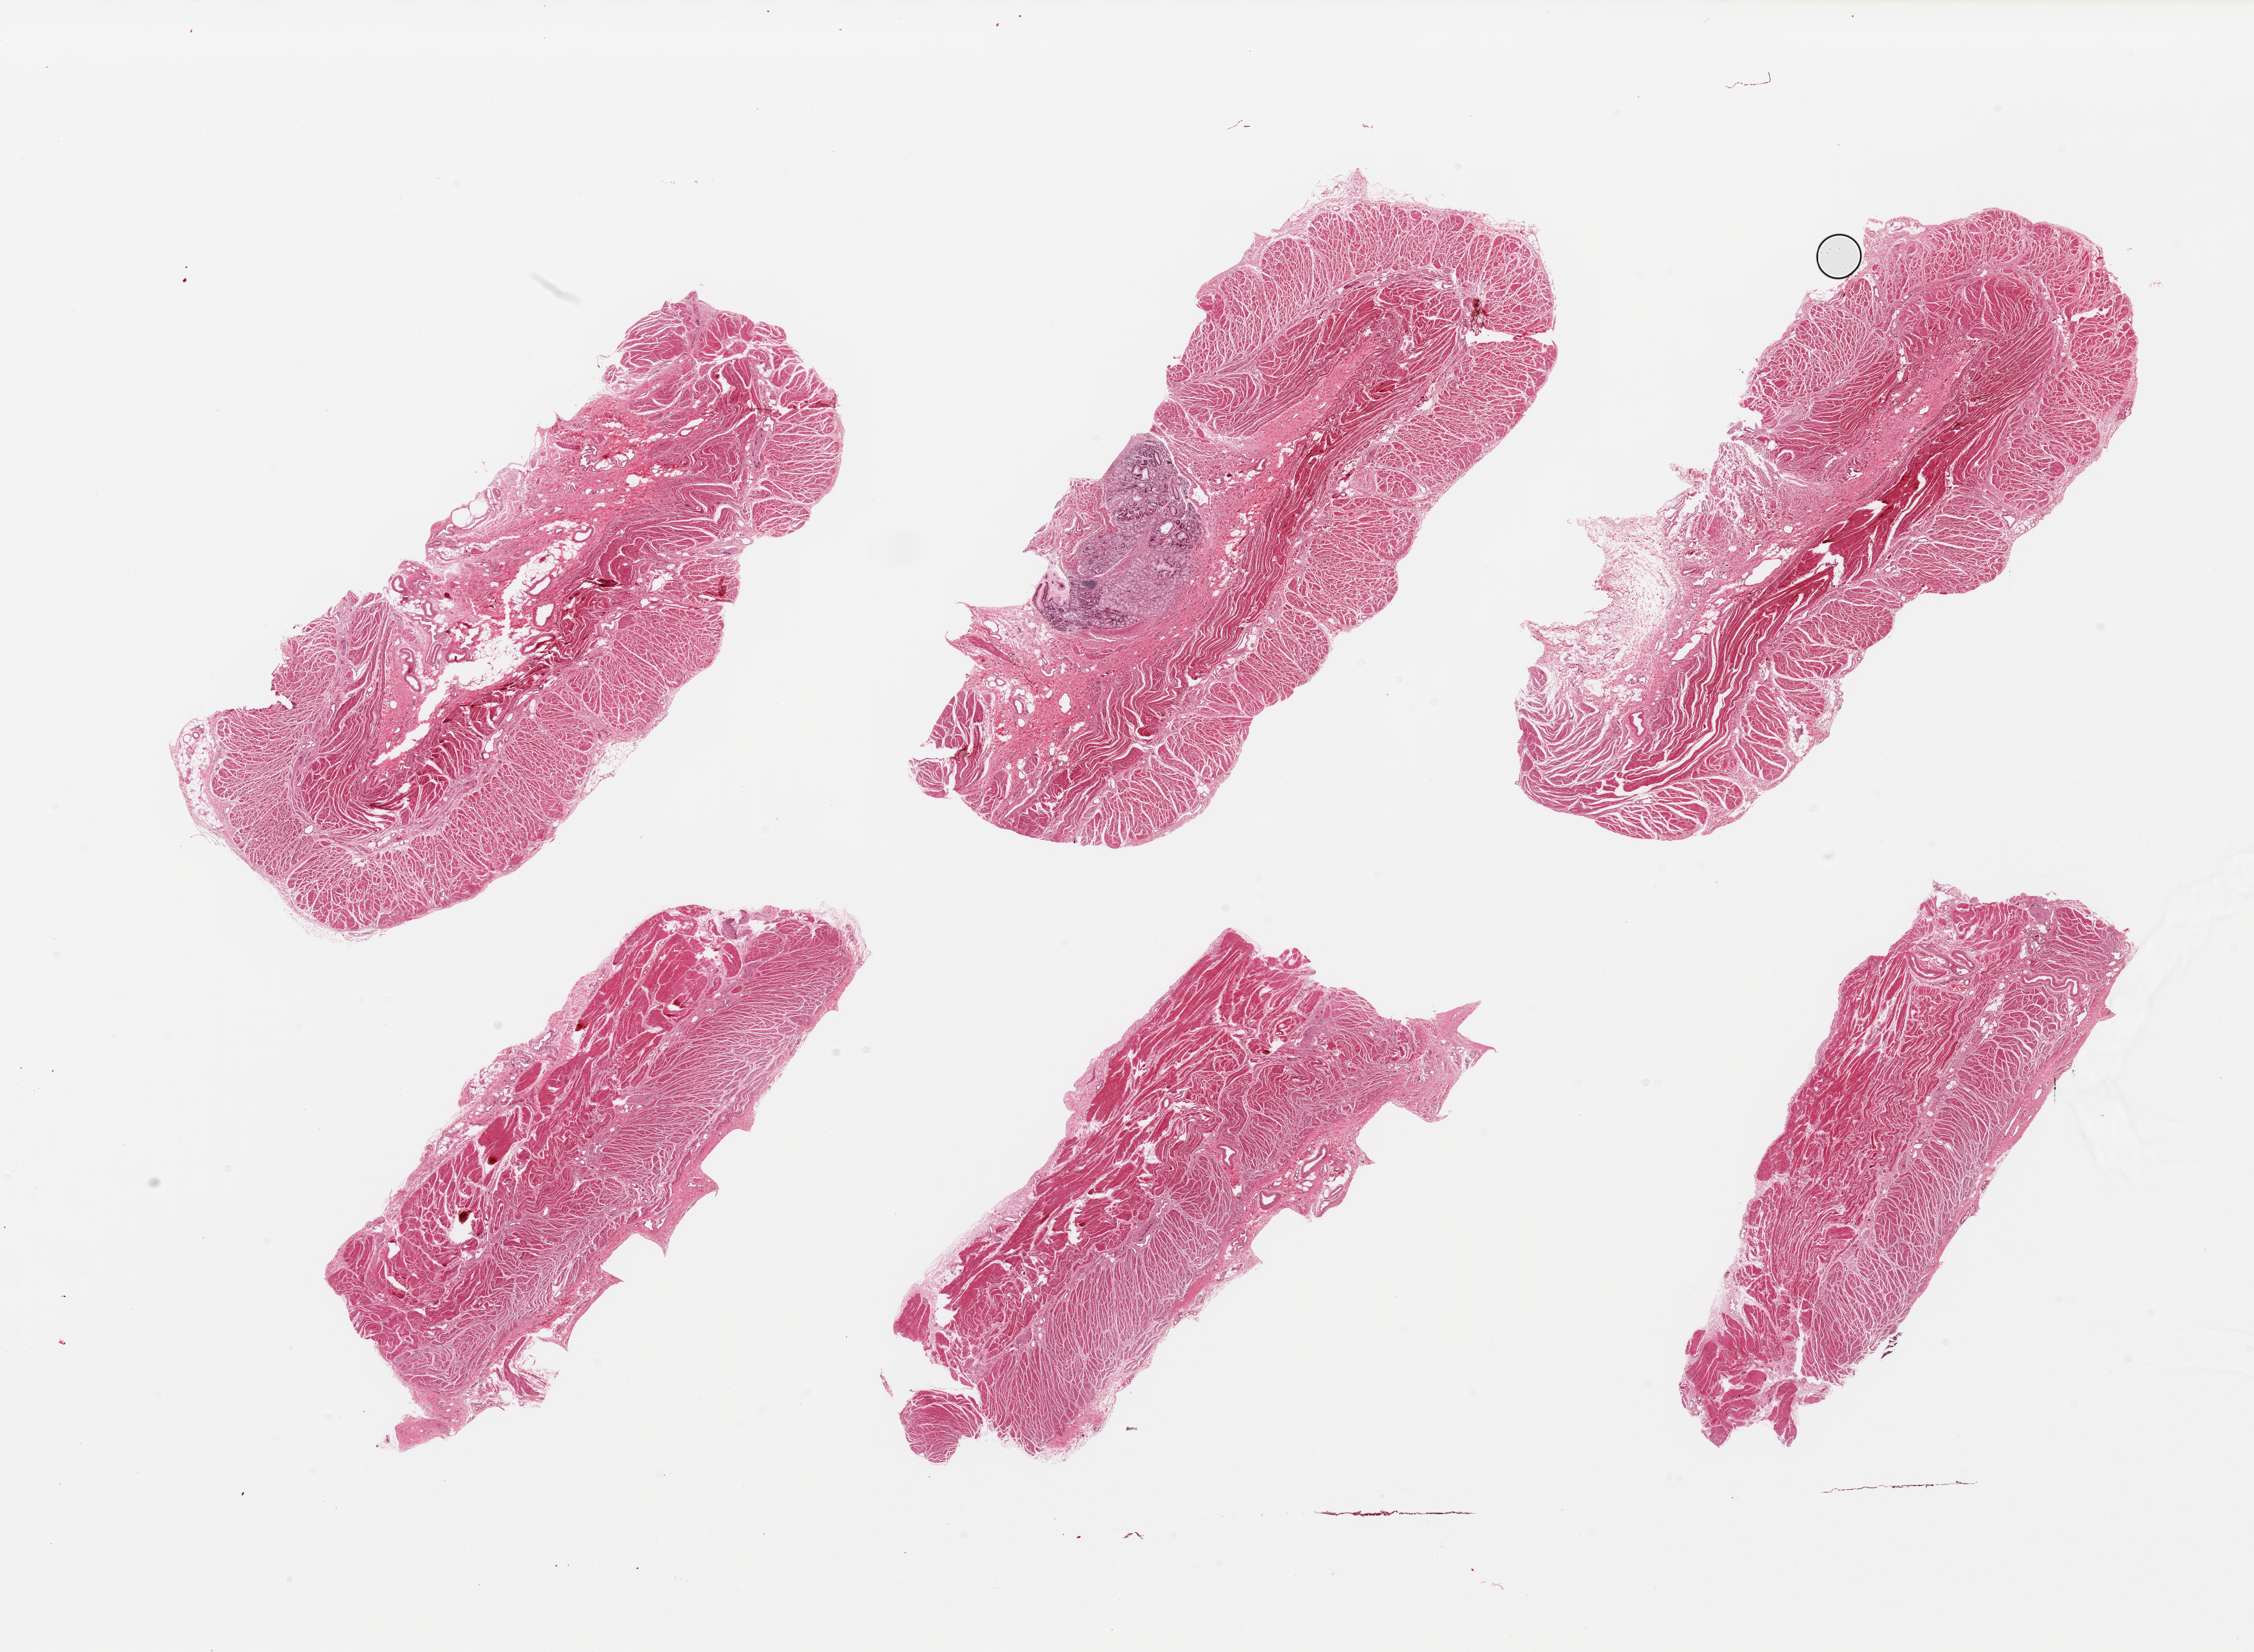
Haematoxylin and eosin whole-slide image, low-resolution overview of the scanned area, about 30.5 x 22.4 mm (from a 20x scan); PAXgene-fixed, paraffin-embedded tissue; section of gastroesophageal junction (target tissue); tissue donor sample. Female donor.
- review note (as recorded): 6 pieces, all muscularis, ~2mm focus heterotopic gastric mucosa, one section